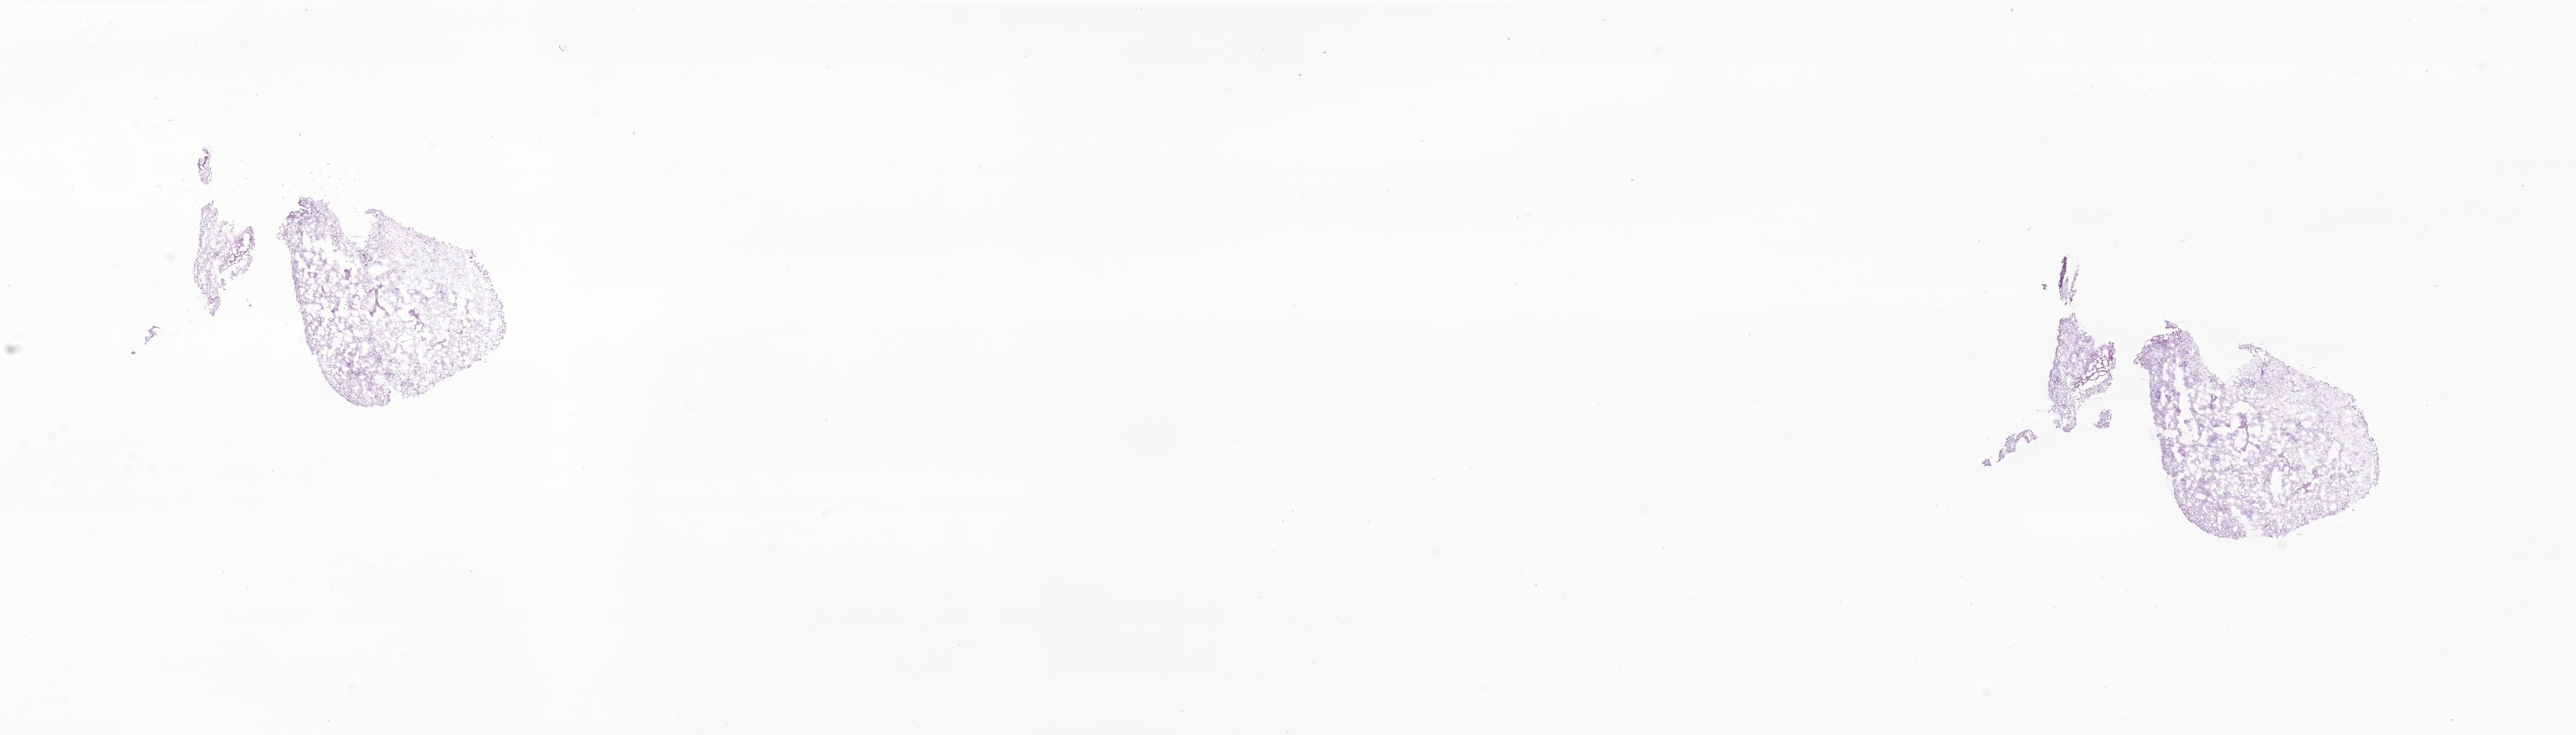
Whole-slide image, H&E stain of tumor tissue from the brain, whole scanned area (about 24.4 x 7.0 mm) shown as a low-resolution overview; cryosection (OCT / tissue freezing medium). Patient: female, age 975 days (about 2.7 years).
Diagnosis (ICD-O-3 morphology term): Pilocytic astrocytoma.